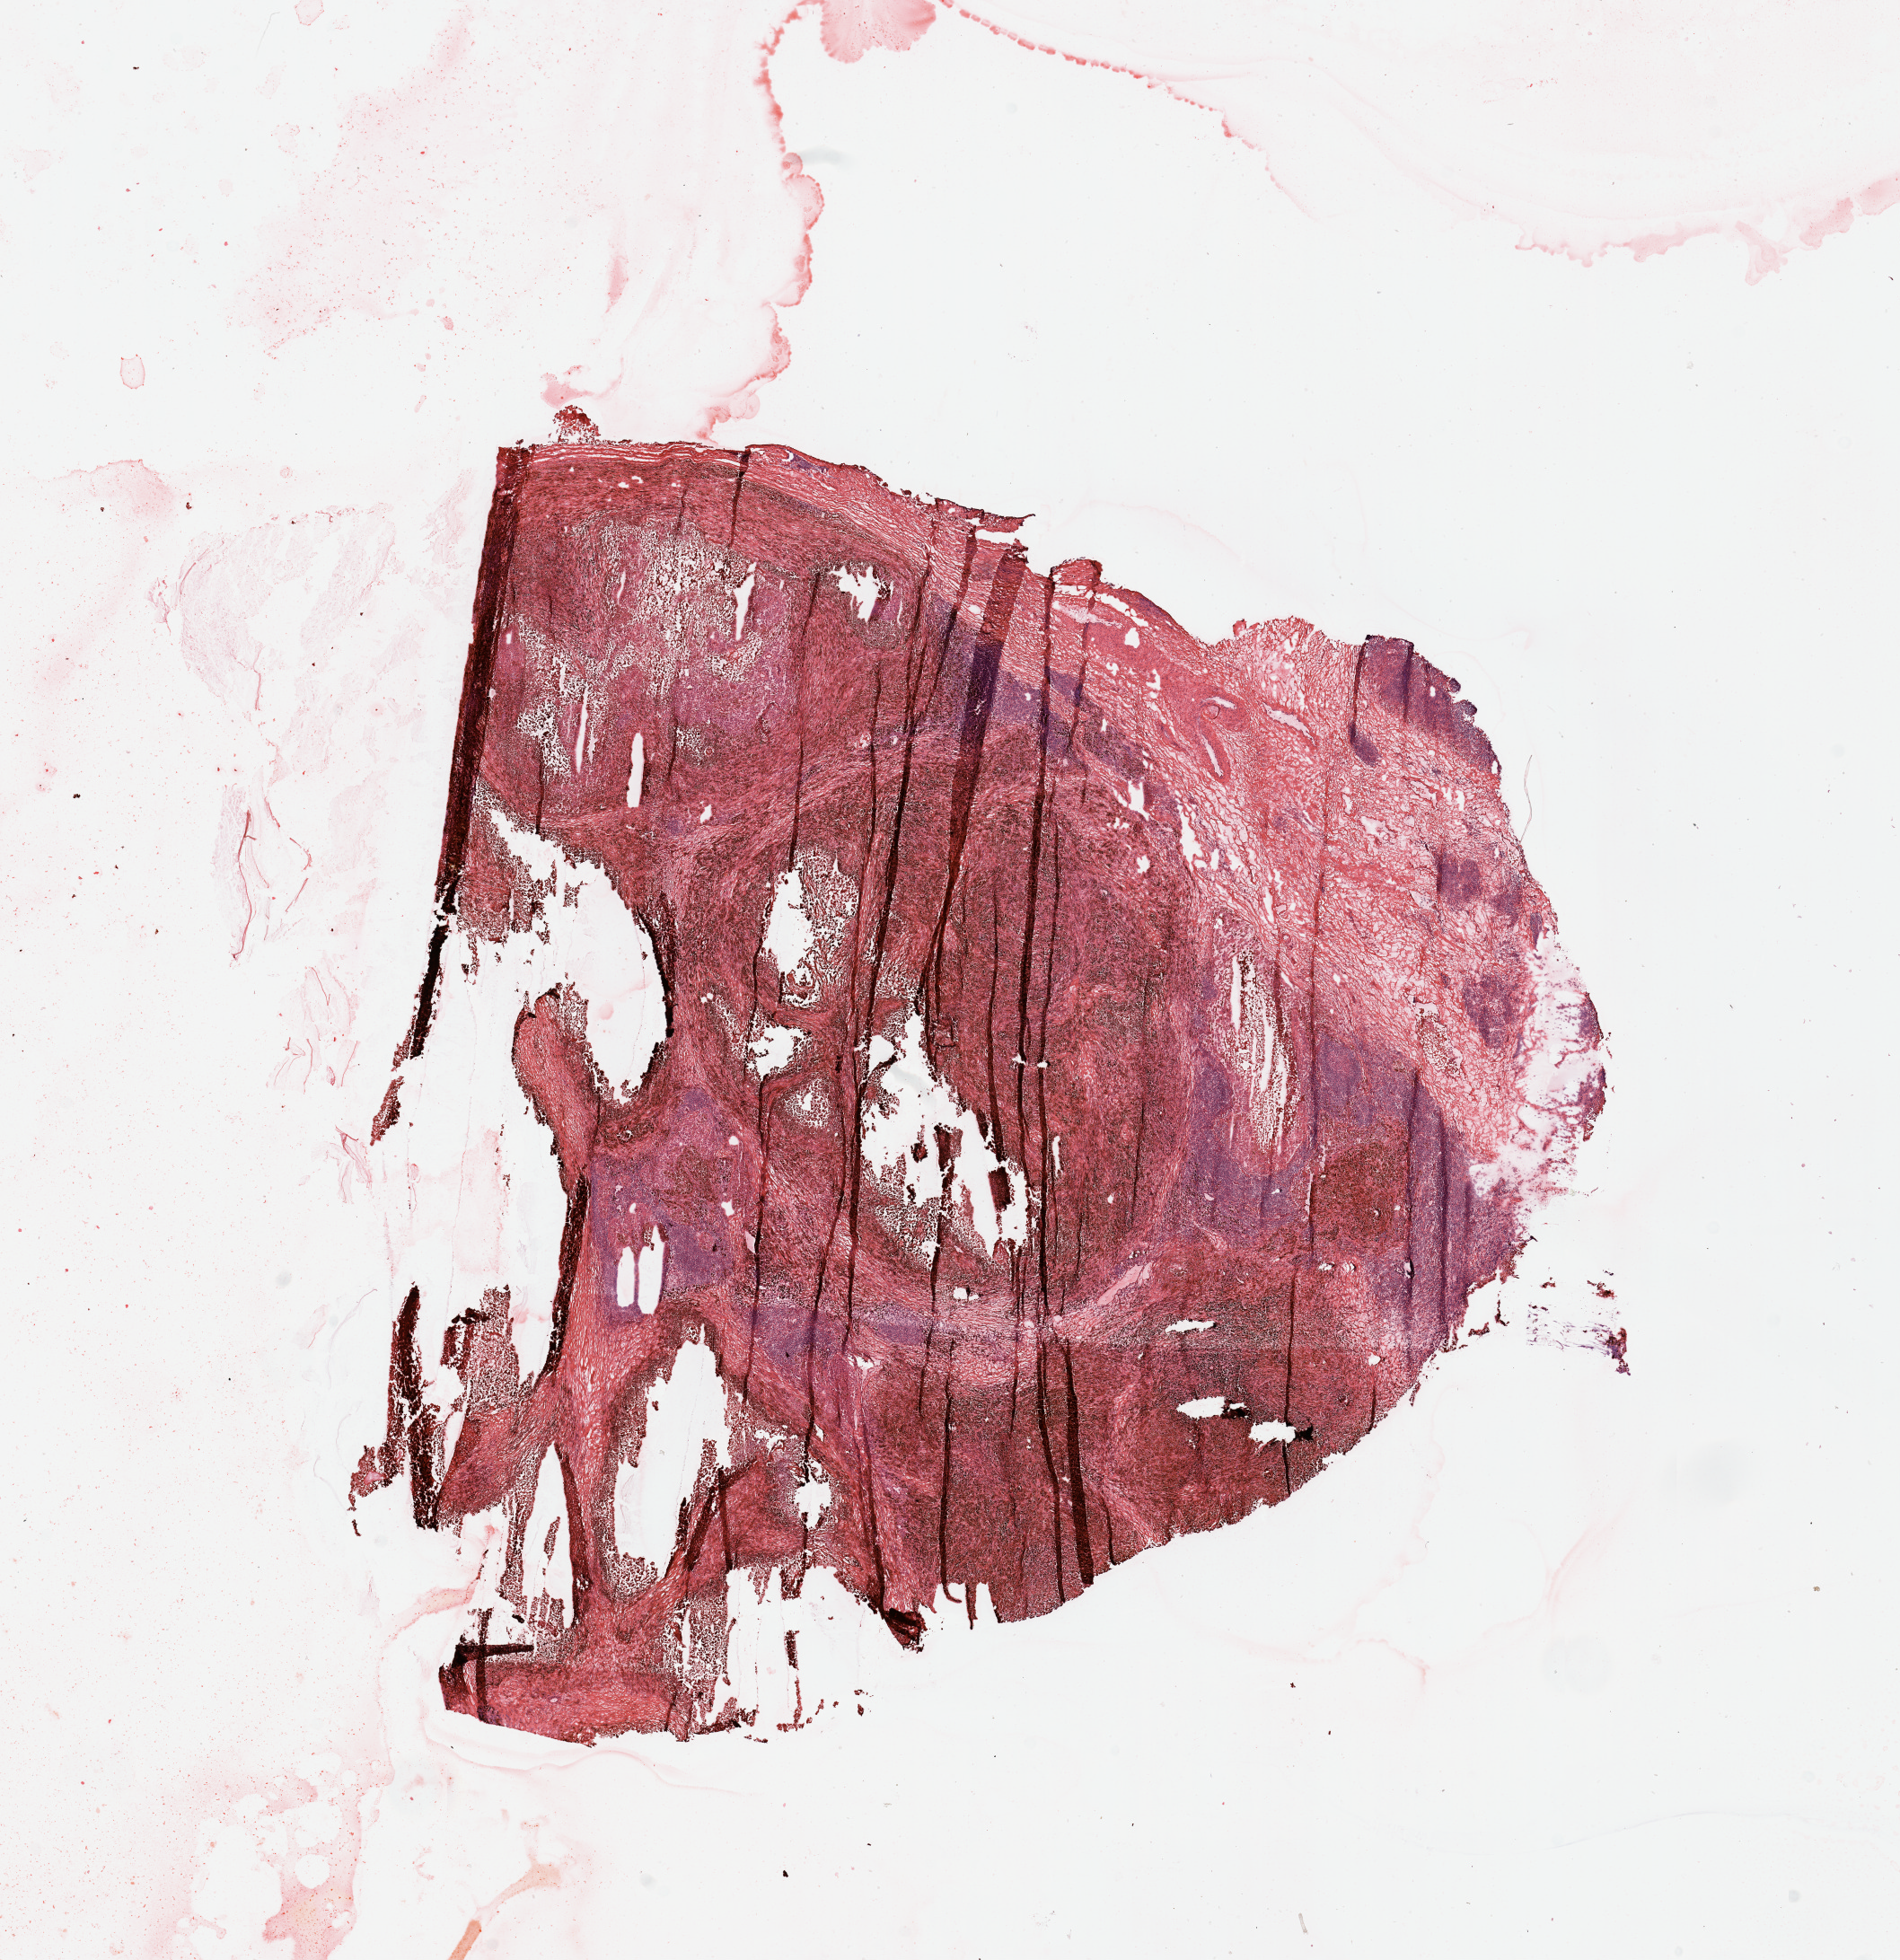
Whole-slide histology image, H&E-stained, a low-resolution overview of the entire scanned area, about 16.7 x 17.3 mm, melanoma tumour tissue; sampled site not recorded. 23-year-old female patient.
Patient diagnosis (cohort enrolment): cutaneous melanoma (skin).